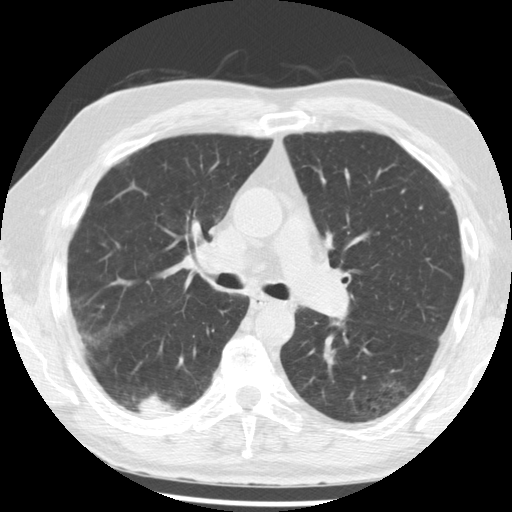
Low-dose screening chest CT, axial slice, third screening round (two years after baseline), lung window (W 1500 / L -600 HU), 2.5 mm slice thickness, standard (soft-tissue) reconstruction kernel (STANDARD), slice 126 of 221 in the series, 512 × 512 image matrix, field of view 350 × 350 mm. Male participant, aged 68 years at enrolment. Current smoker at enrolment.
Lesion marked by an expert reader, bounding box (x1, y1, x2, y2) in pixels: (118, 378, 193, 432). The screening reader recorded 3 non-calcified nodules or masses ≥4 mm on this exam; which of them this box marks is not recorded. Lung cancer was diagnosed 48 days after this screen: squamous cell carcinoma, NOS, right lower lobe, moderately differentiated (G2), stage IB (AJCC 6th edition), 20 mm at pathology.